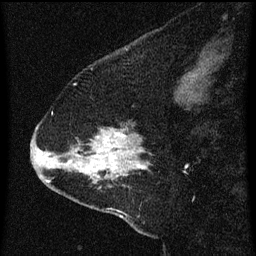
Breast MRI (dynamic contrast-enhanced), one sagittal slice; slice 16 of 60 in the series (ordered by position); dynamic contrast-enhanced series, image 2 of 3 at this slice position (ordered by acquisition); 1.5 T; TE 4.2 ms, TR 8 ms; 2 mm slice thickness; 256 × 256 image matrix, field of view 180 × 180 mm. Female patient, age 47 years.
Outlined on this slice (semi-automatic segmentation, software-assisted and operator-edited):
- analysis volume of interest (the breast-tissue region the enhancement analysis was run in; not a lesion): box from (x=36, y=114) to (x=153, y=213) px
- tumour enhancement mask (voxels above the 70 % enhancement threshold inside the analysis volume of interest): (x=47, y=130)–(x=145, y=183)